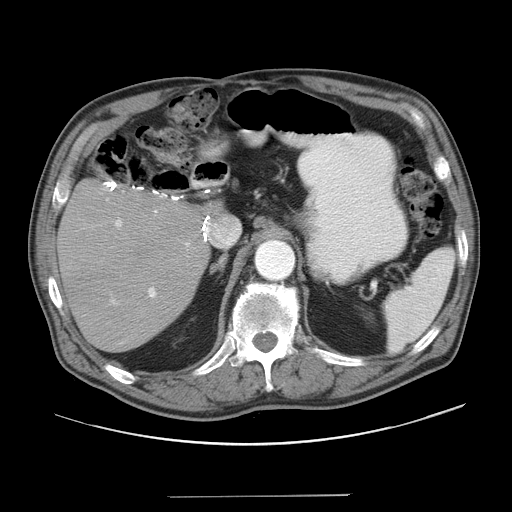
Contrast-enhanced abdominal CT, one axial slice. Slice 27 of 41 in the series (ordered by position). Reconstruction kernel STANDARD. 120 kVp. Intravenous contrast given. Soft-tissue window (W 400 / L 40 HU). 512 × 512 image matrix, field of view 420 × 420 mm. Male patient, age 75 years. From the clinical record (not read from this slice): diagnosis: colorectal cancer liver metastases, imaged before liver resection; multiple liver metastases: no; largest metastasis: 5.2 cm; chemotherapy before resection: no.
Structures marked on this image (manually delineated by an expert):
- liver: box from (x=60, y=185) to (x=208, y=351) px
- planned liver remnant (the part of the liver to remain after resection): (x=60, y=186)–(x=207, y=351)
- portal vein (with intrahepatic branches): (x=110, y=209)–(x=191, y=305)